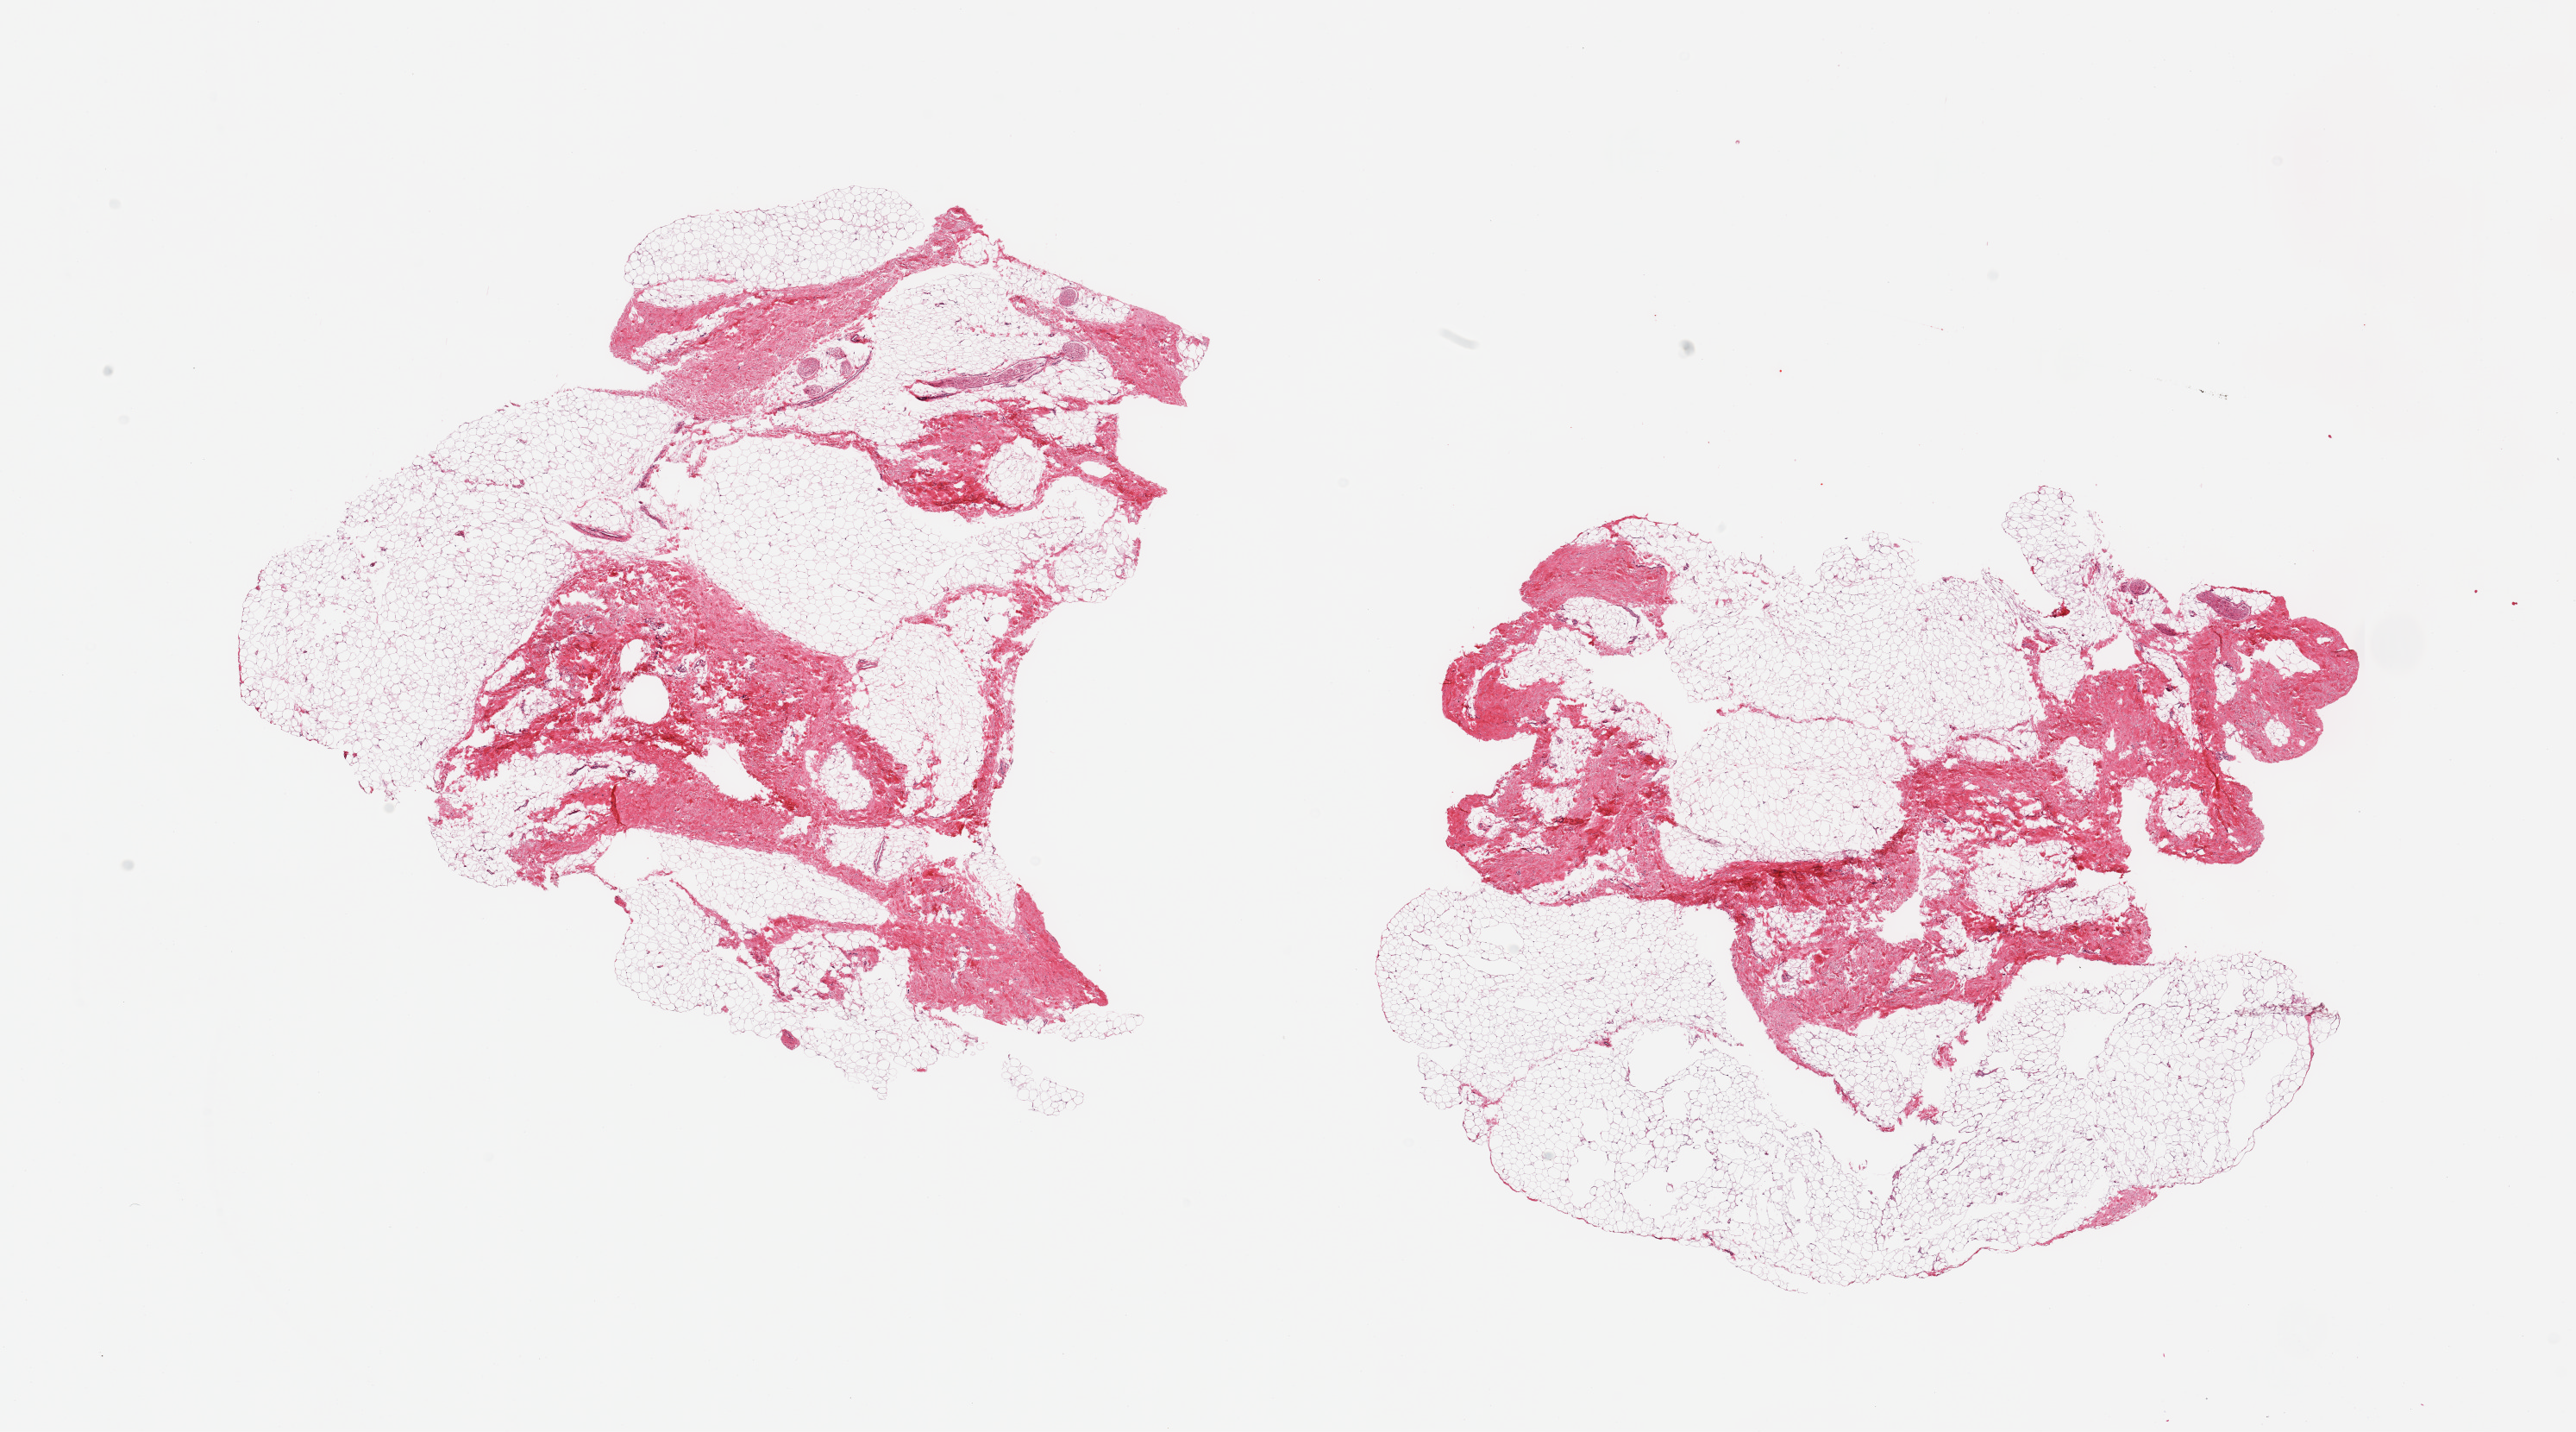
Digitized haematoxylin and eosin-stained section — whole scanned area (about 23.6 x 13.1 mm) shown as a low-resolution overview. PAXgene-fixed, paraffin-embedded tissue. Sampled site (target tissue): breast. Donor tissue sample.
Review note (as recorded): 2 pieces; fibroadipose tissue devoid of mammary parenchyma (in these cuts).